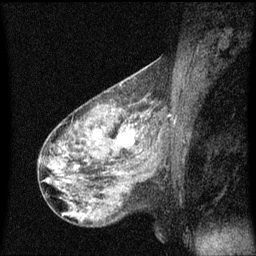
Breast MRI (dynamic contrast-enhanced), one sagittal slice. Position 37 of 60 along the scan axis. Dynamic contrast-enhanced series, image 2 of 3 at this slice position (ordered by acquisition). 1.5 T. TE 4.2 ms, TR 8 ms. 256 × 256 image matrix, field of view 200 × 200 mm. Patient: female, 50 years.
Structures marked on this image (semi-automatically segmented with operator editing):
- analysis volume of interest (the breast-tissue region the enhancement analysis was run in; not a lesion): bounding box <106,118,148,159> (left, top, right, bottom; pixels)
- tumour enhancement mask (voxels above the 70 % enhancement threshold inside the analysis volume of interest): <117,128,134,147>